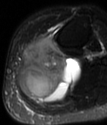
MRI of an extremity soft-tissue mass, one axial slice; slice 37 of 78 in the series (ordered by position); T2-weighted fat-saturated; MR volume resampled by the dataset authors to the PET/CT grid (not the native acquisition matrix); 3.27 mm slice thickness; 107 × 125 image matrix, field of view 104 × 122 mm. Female patient. From the clinical record (not read from this slice): histological type: extraskeletal high grade osteogenic sarcoma; grade: high; site of the primary tumour: left calf.
Structures marked on this image (expert contour drawn on MRI and transferred to this co-registered scan by the dataset authors):
- gross tumour volume (mass): bounding box (x1, y1, x2, y2) in pixels: (19, 36, 81, 103)